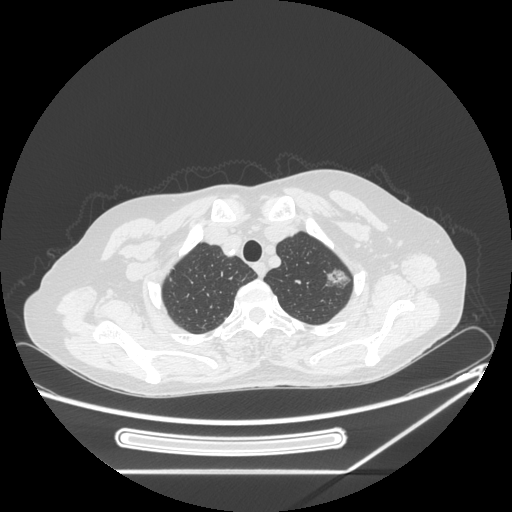
Chest CT, one axial slice. Position 209 of 250 along the scan axis. 120 kVp. Lung window (W 1500 / L -600 HU). 1.25 mm slice thickness. 512 × 512 image matrix, field of view 409 × 409 mm. Female patient, age 57 years. Case-level facts recorded for this patient, not image findings: clinical TNM (as recorded): T1c N0 M0; histopathological grade: G2-3.
Annotated regions visible in this slice (rectangle marked by the reading radiologist):
- lung tumour (recorded histology: adenocarcinoma): box from (x=321, y=263) to (x=351, y=292) px